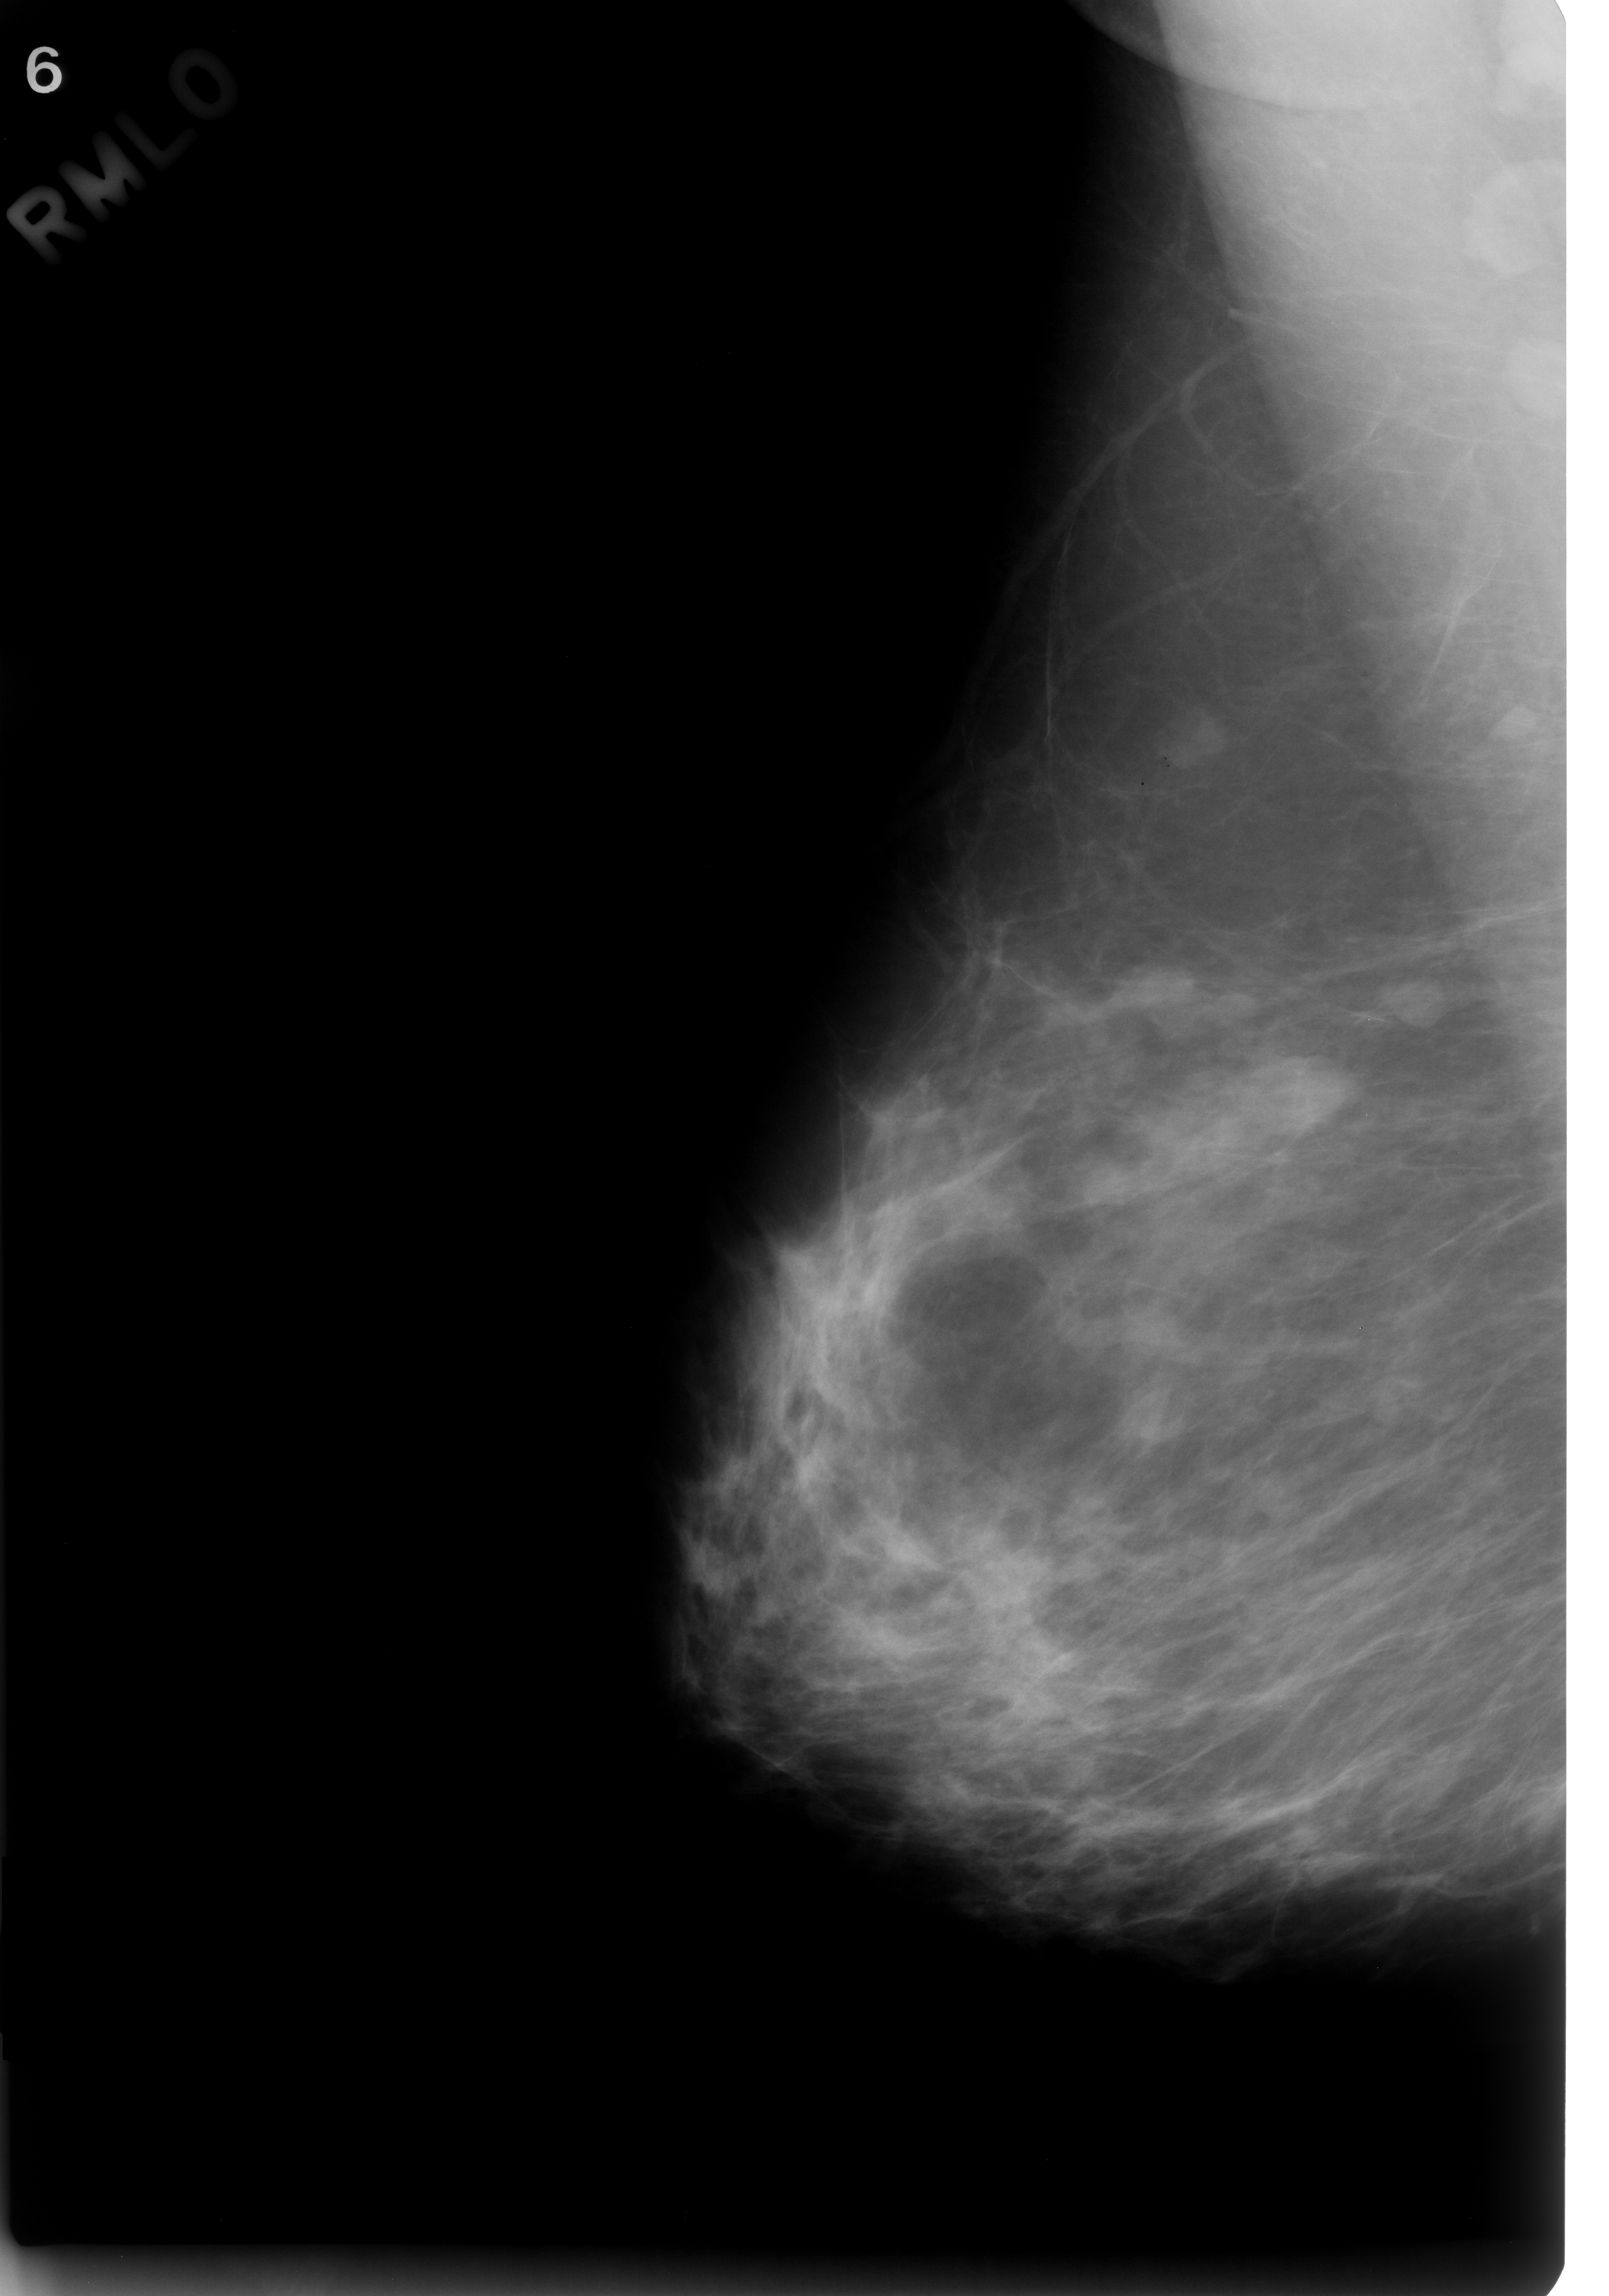
Scanned film-screen mammogram, right breast, MLO view, breast composition: scattered fibroglandular densities (BI-RADS density category 2 of 4).
Radiologist-marked abnormalities on this image: Finding 1 of 3: mass, shape lobulated, margins circumscribed; BI-RADS assessment category 3; pathology result (as recorded, not read from the image): benign. Finding 2 of 3: mass, shape round, margins circumscribed; BI-RADS assessment category 3; subtlety rating 5 on a 1 (subtle) to 5 (obvious) scale; pathology (as recorded): benign. Finding 3 of 3: mass, shape lobulated, margins microlobulated; BI-RADS assessment category 3; pathology (as recorded): benign.